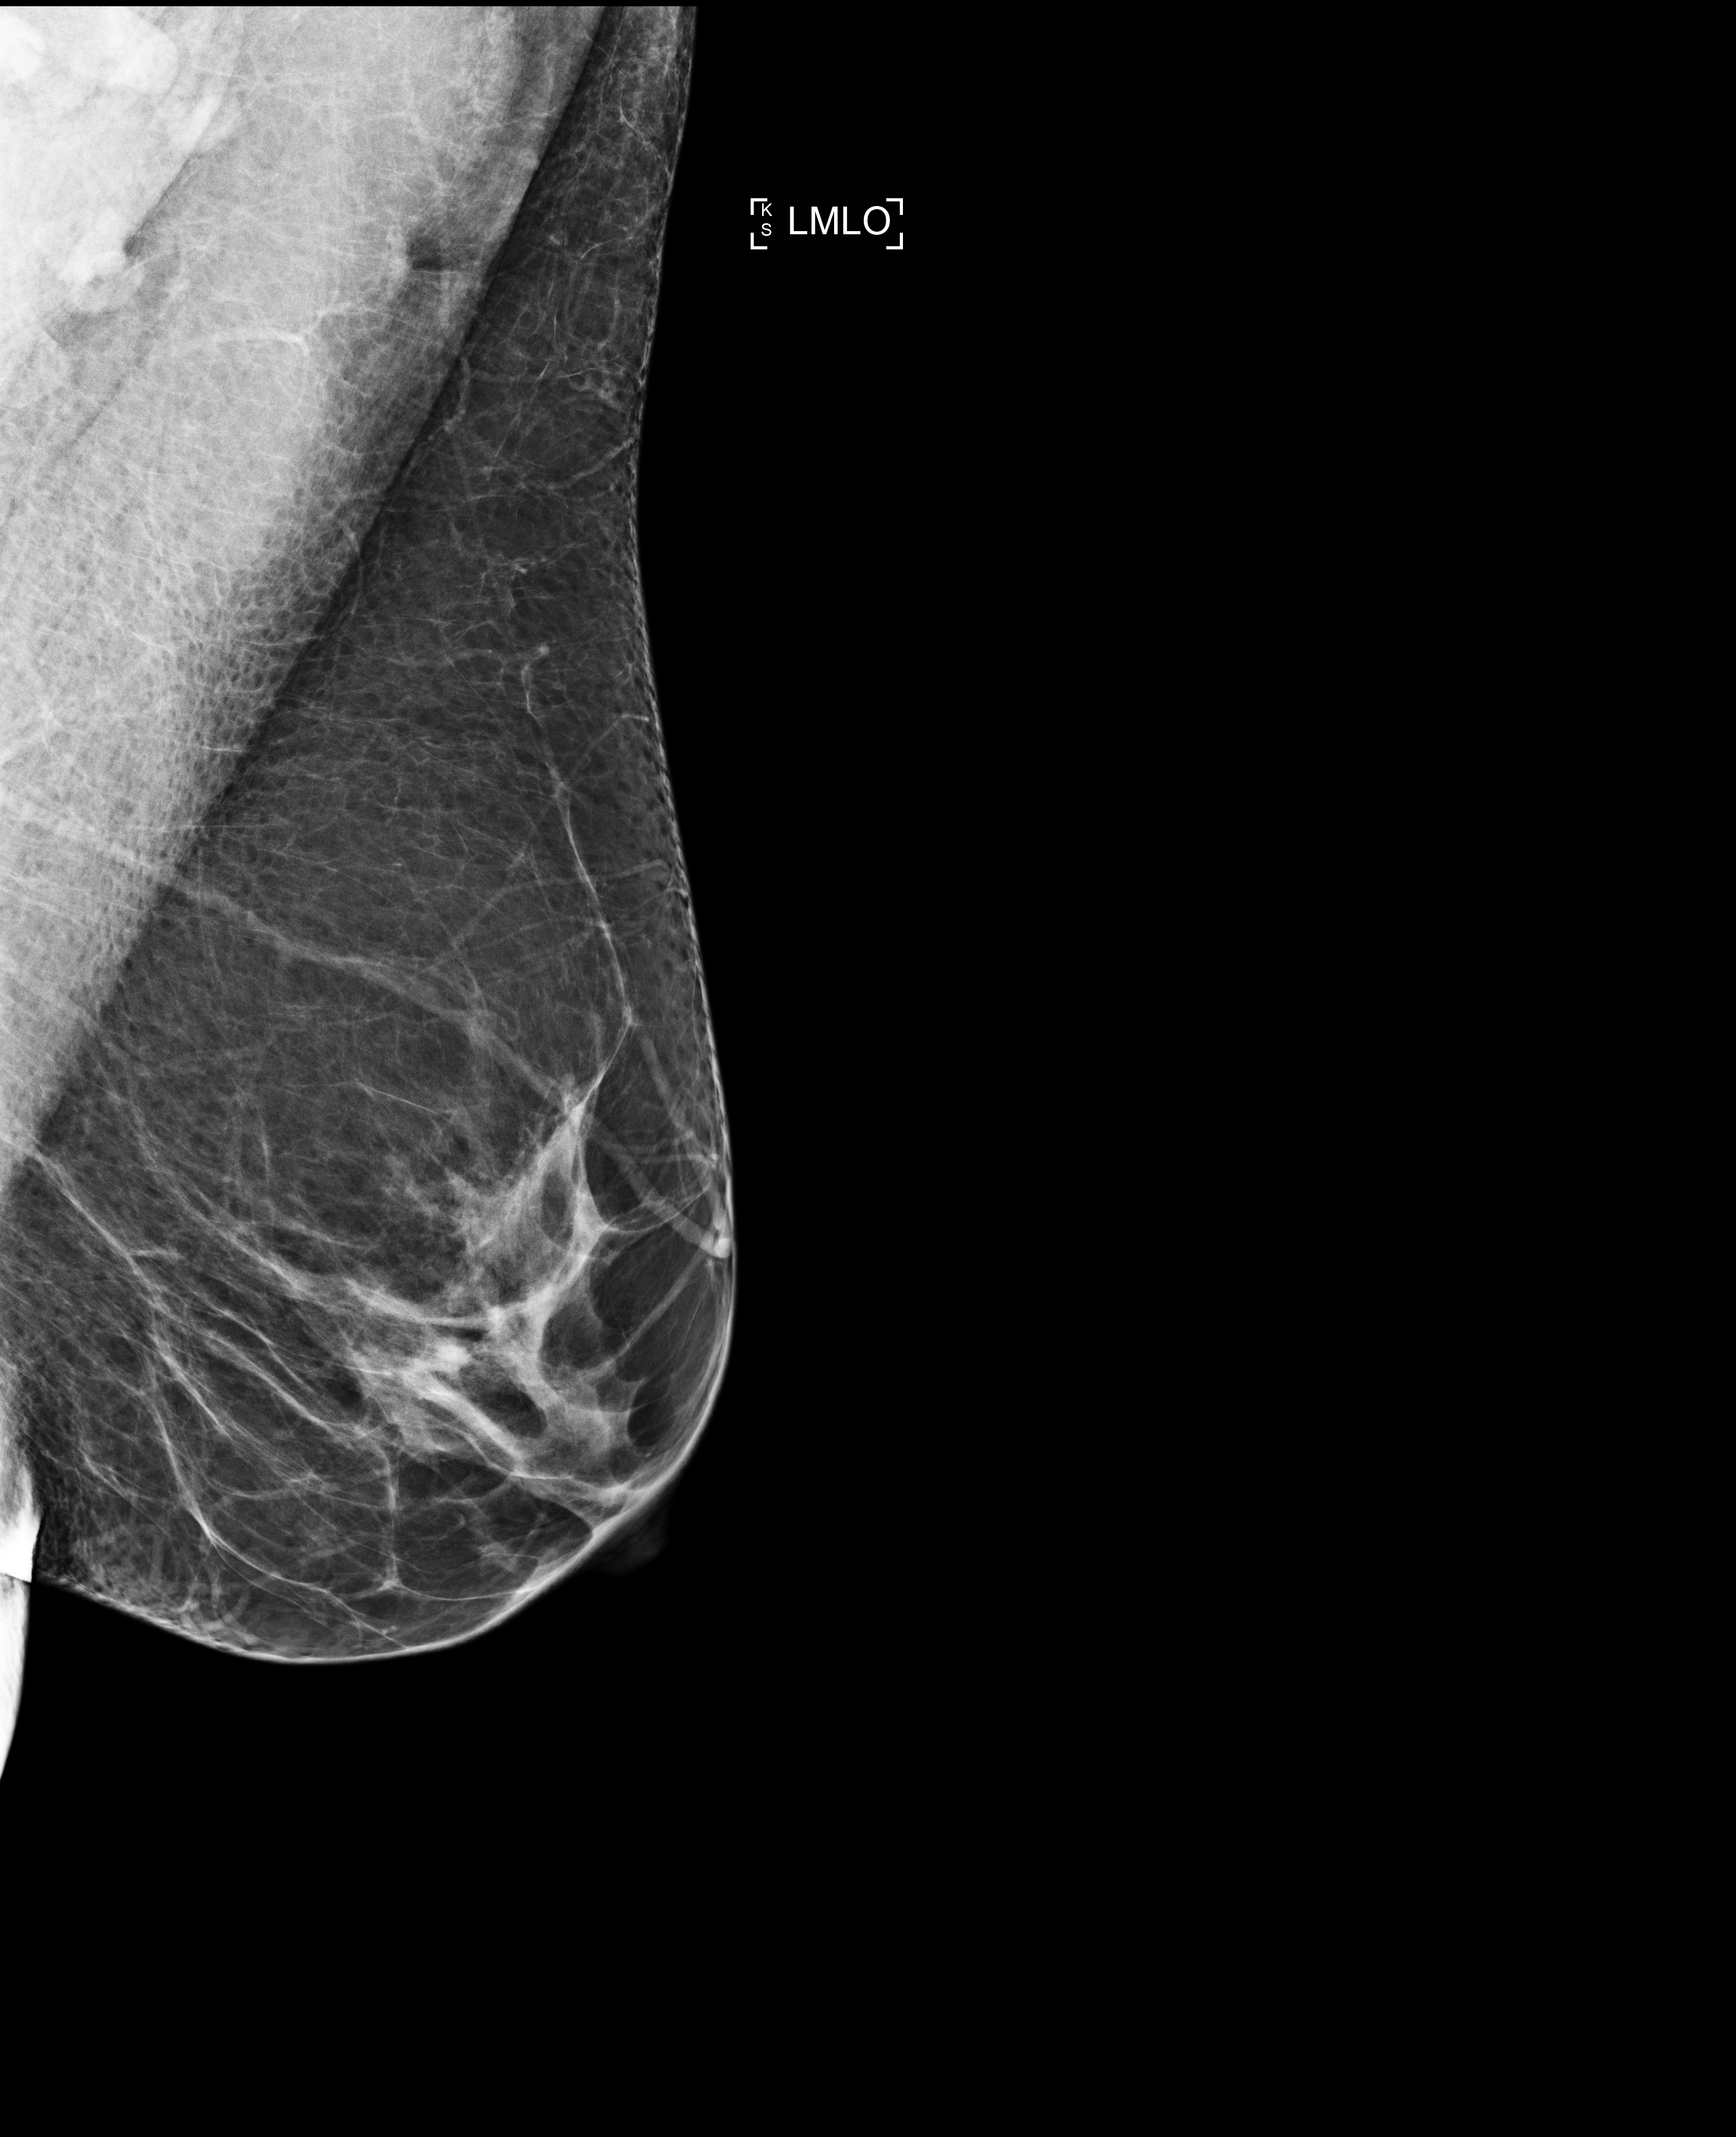
Full-field digital mammogram (FFDM), left breast, medio-lateral oblique projection, diagnostic examination (additional views). Female patient, age 49 years.
Breast density at the screening exam (both breasts): heterogeneously dense (BI-RADS density category c). Final BI-RADS assessment for this screening round (tomosynthesis exam, both breasts): category 2. Recall: recalled for additional imaging after this screen.